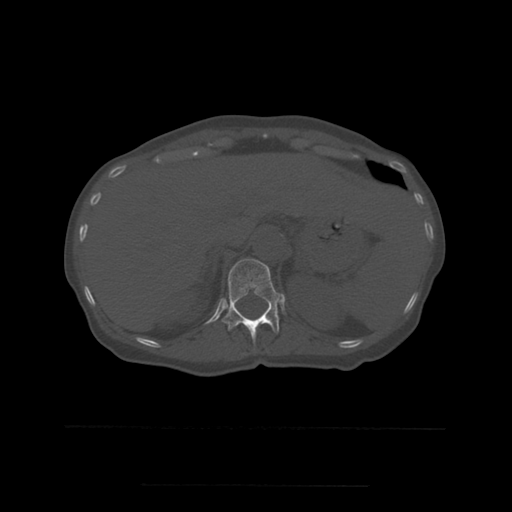
CT including the spine, one axial slice; position 260 of 544 along the scan axis; bone window (W 1800 / L 400 HU); 512 × 512 image matrix, field of view 350 × 350 mm. Patient age 58 years. From the clinical record (not read from this slice): primary cancer: lung.
Annotated regions visible in this slice (semi-automatically segmented with operator editing):
- T12 vertebra: bounding box <222,259,283,343> (left, top, right, bottom; pixels)